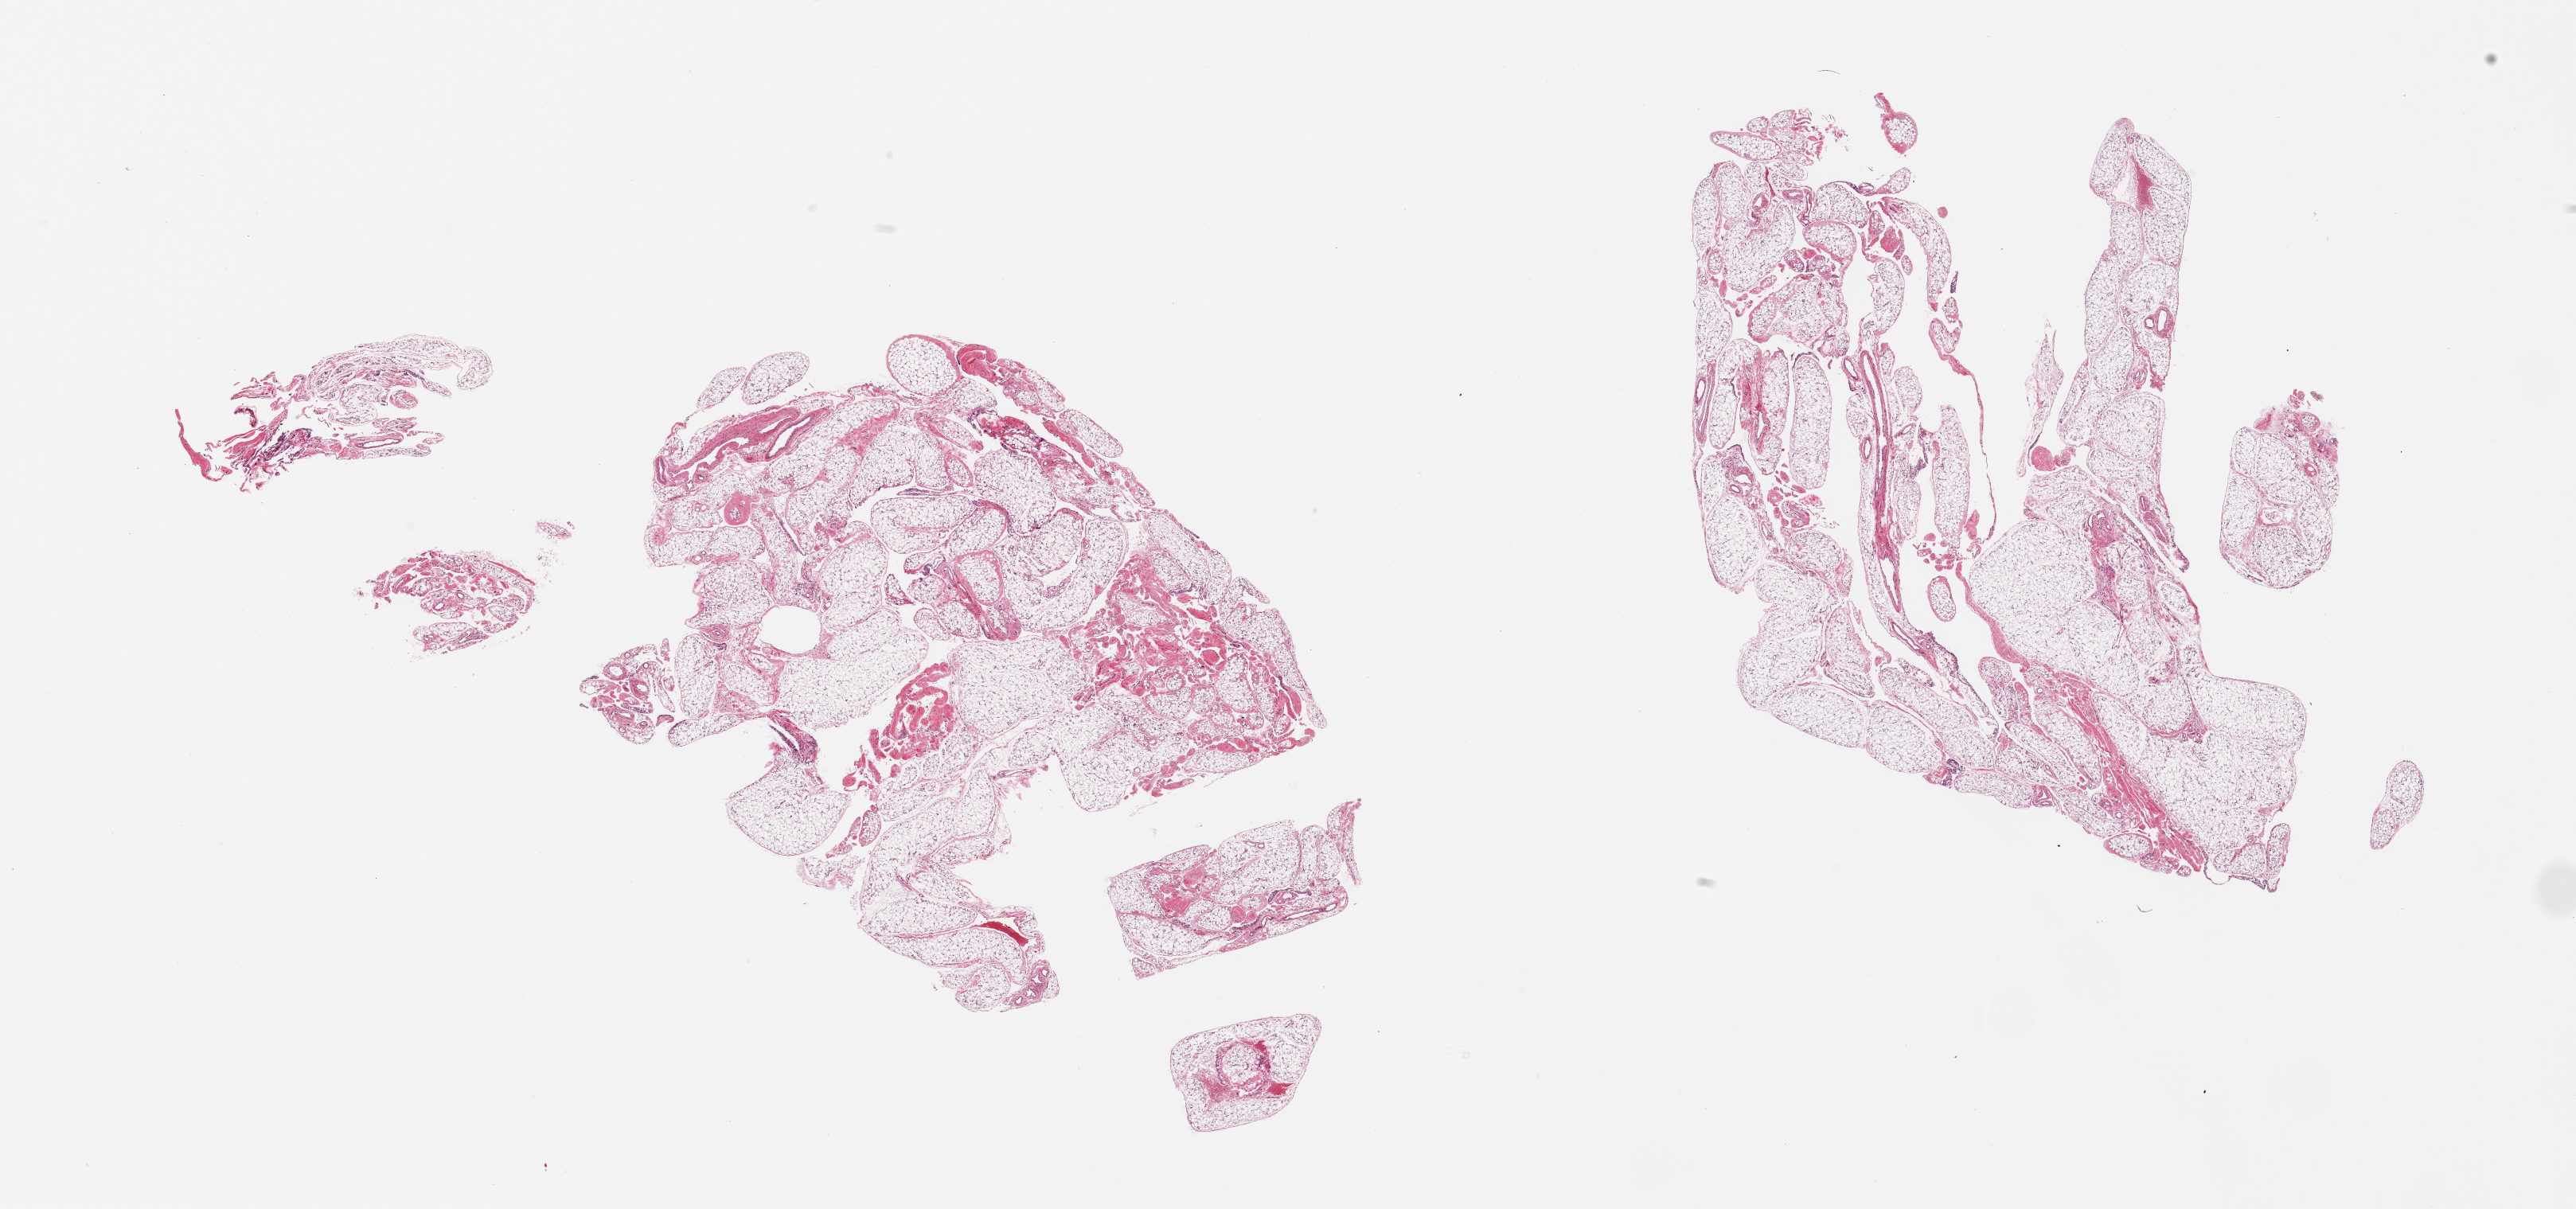
H&E whole-slide image, brightfield — whole scanned area (about 25.6 x 12.0 mm, slide scanned at 20x) shown as a low-resolution overview. PAXgene-fixed, paraffin-embedded tissue. Sampled site (target tissue): omentum. Tissue donor sample. Donor sex: male.
- reviewer comment on this tissue sample: 2 pieces, ~20-30% fascia/vascular elements